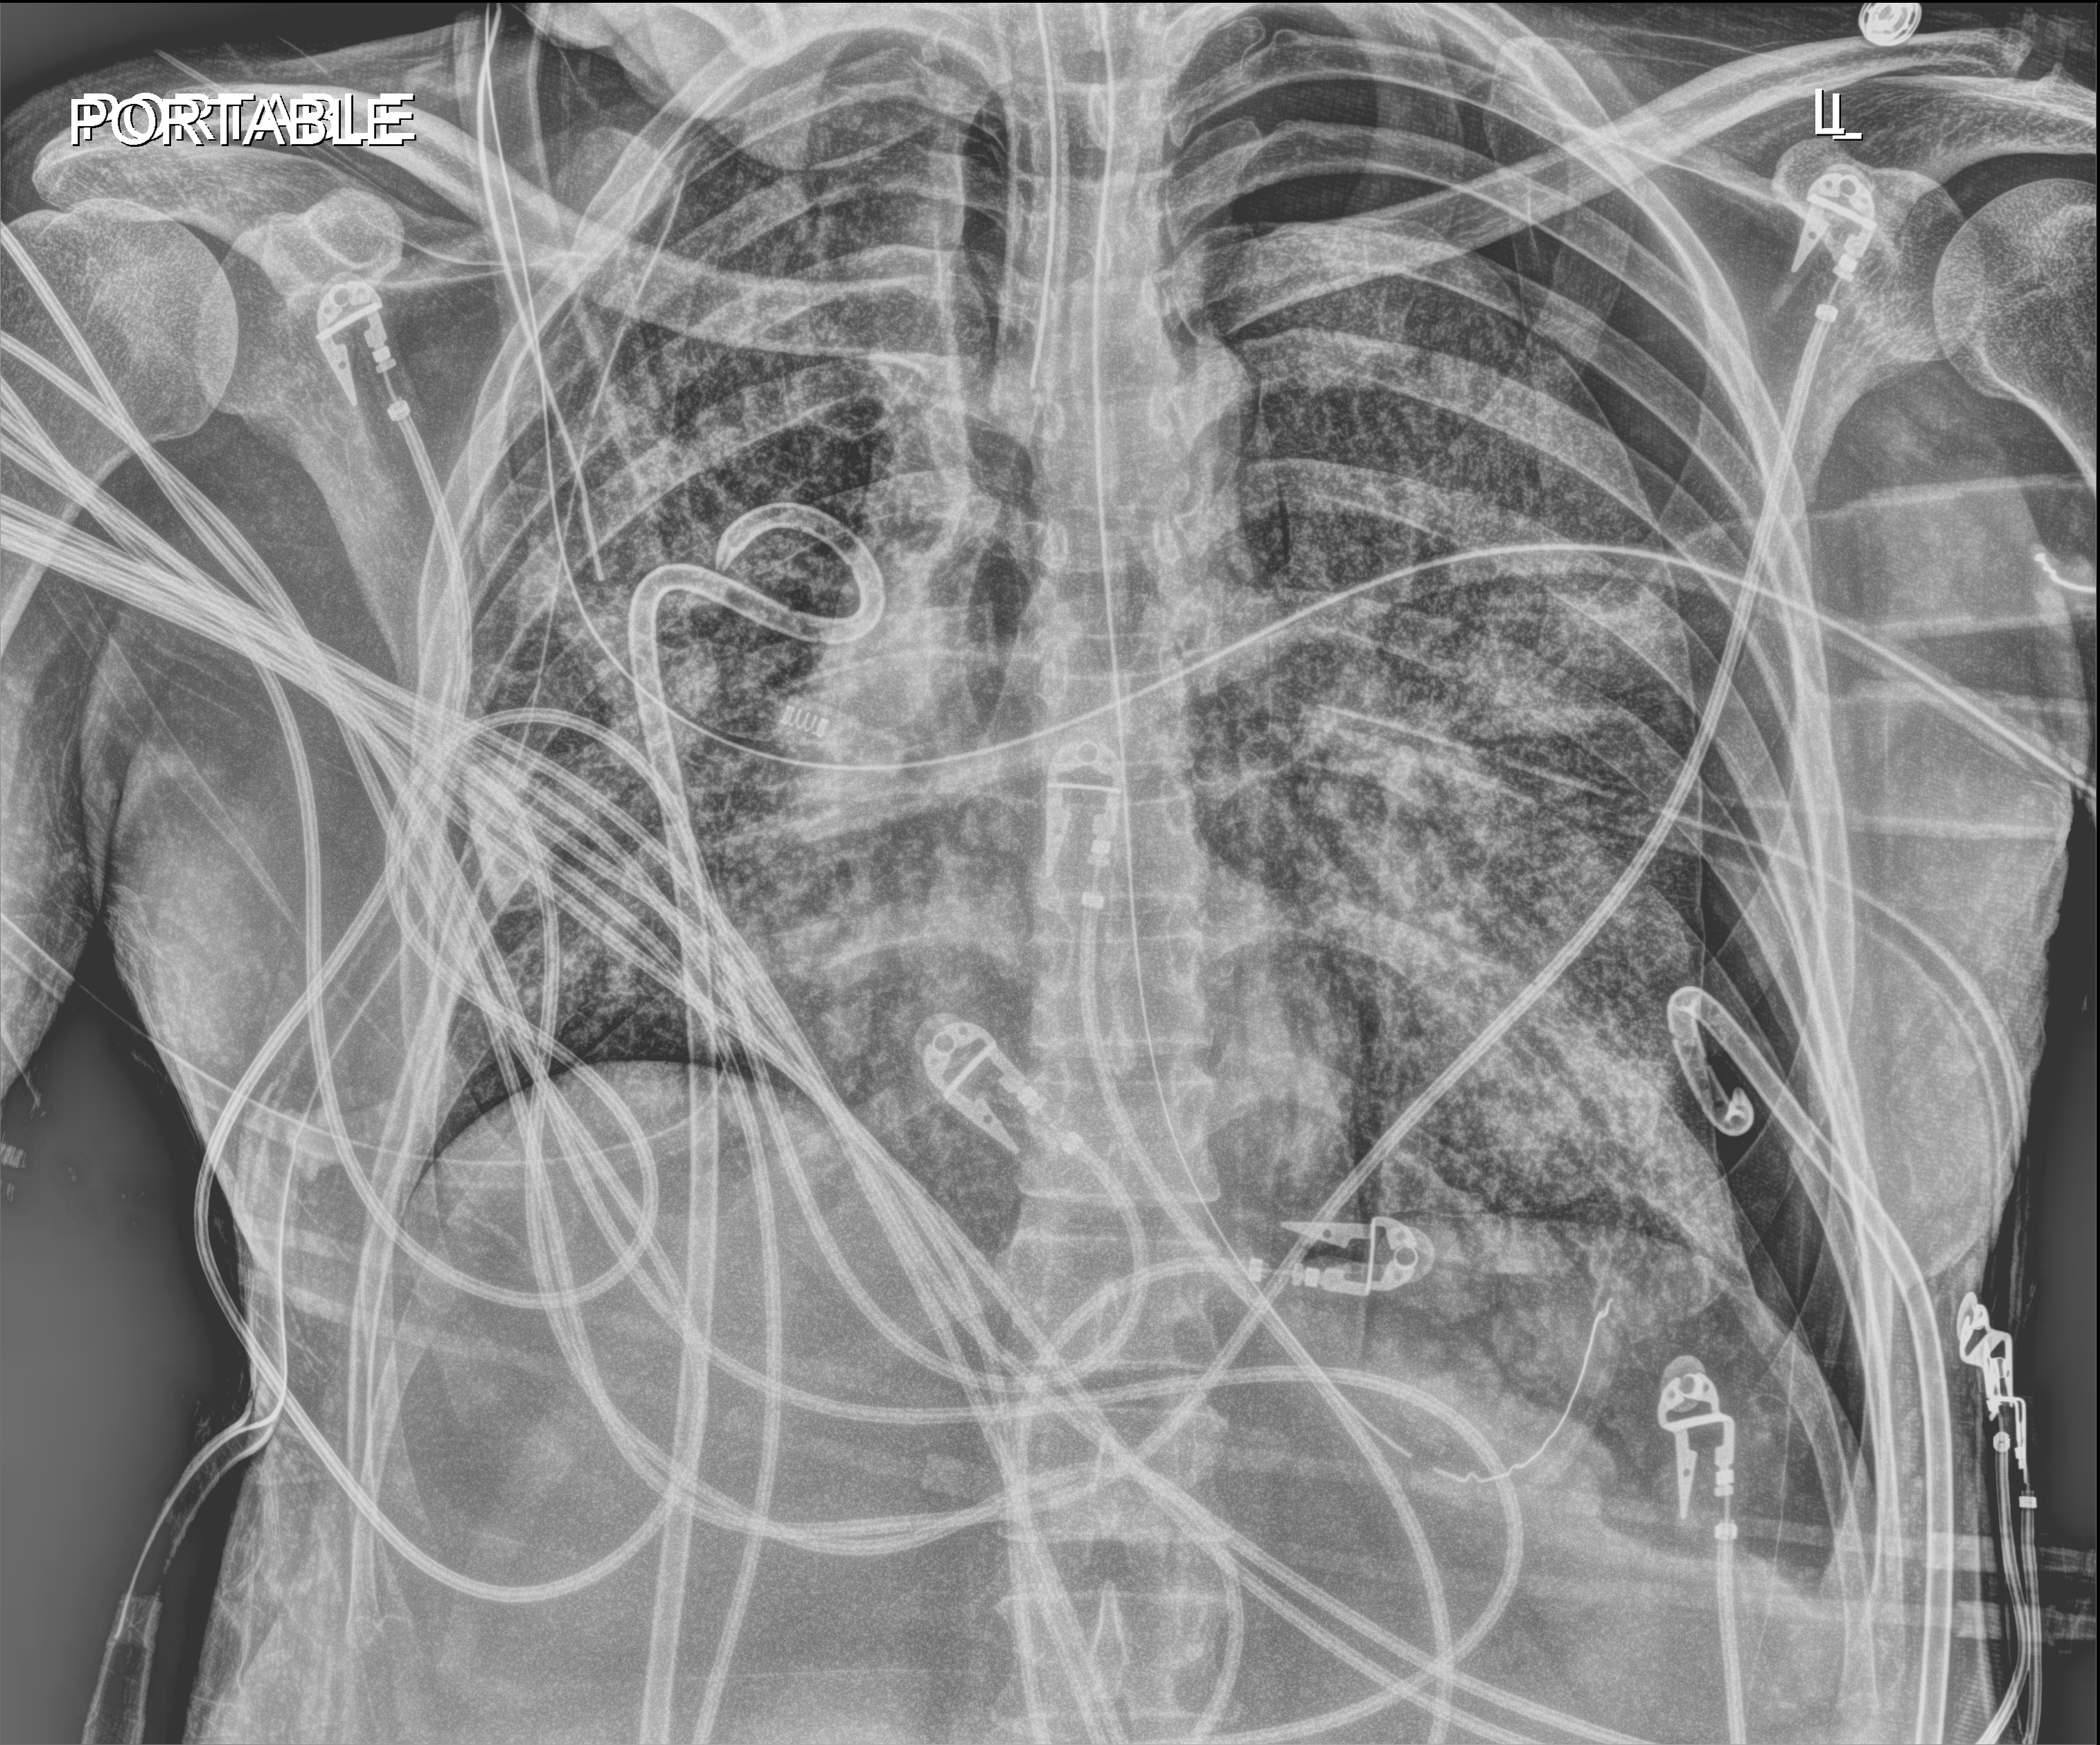
Chest radiograph (digital radiography); anteroposterior (AP) projection. Patient hospitalised with COVID-19, aged 18–59 years.
Hospital-stay facts (about this admission, not read from this image; timing relative to this image not recorded): smoking status (admission record): never; admitted to intensive care during this hospital stay: yes; diabetes (admission record): no.